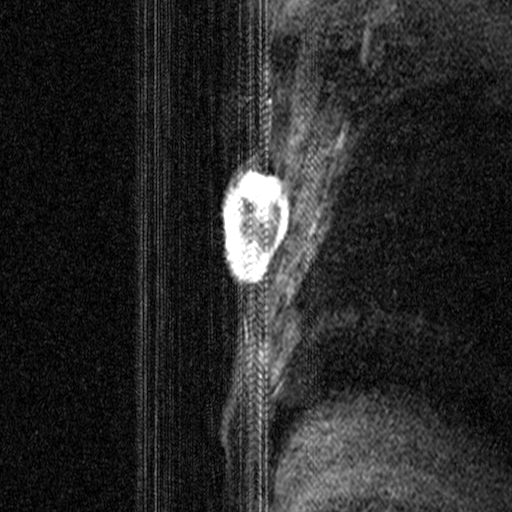
Breast MRI (dynamic contrast-enhanced), one sagittal slice. Slice 28 of 44 in the series (ordered by position). Dynamic contrast-enhanced study with each time point stored as its own series, time point 2 of 3 at this slice position (early post-contrast, ordered by acquisition time). 1.5 T. TE 4.5 ms, TR 11 ms. 512 × 512 image matrix, field of view 200 × 200 mm. Female patient, age 44 years. From the clinical record (not read from this slice): setting: breast cancer imaged before/during neoadjuvant chemotherapy; receptor status: HR-positive, HER2-negative.
Outlined on this slice (semi-automatically segmented with operator editing):
- analysis volume of interest (the breast-tissue region the enhancement analysis was run in; not a lesion): bounding box [x1, y1, x2, y2] px = [206, 164, 292, 299]
- tumour enhancement mask (voxels above the 90 % enhancement threshold inside the analysis volume of interest): [224, 165, 289, 281]